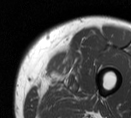
MRI of an extremity soft-tissue mass, one axial slice; slice 12 of 55 in the series (ordered by position); MR volume resampled by the dataset authors to the PET/CT grid (not the native acquisition matrix); 3.27 mm slice thickness; 131 × 118 image matrix, field of view 128 × 115 mm. Male patient. Case-level facts recorded for this patient, not image findings: histological type: pleiomorphic liposarcoma; grade: high; site of the primary tumour: left thigh.
Annotated regions visible in this slice (expert contour drawn on MRI and transferred to this co-registered scan by the dataset authors):
- gross tumour volume including surrounding oedema: bounding box [x1, y1, x2, y2] px = [55, 66, 88, 99]